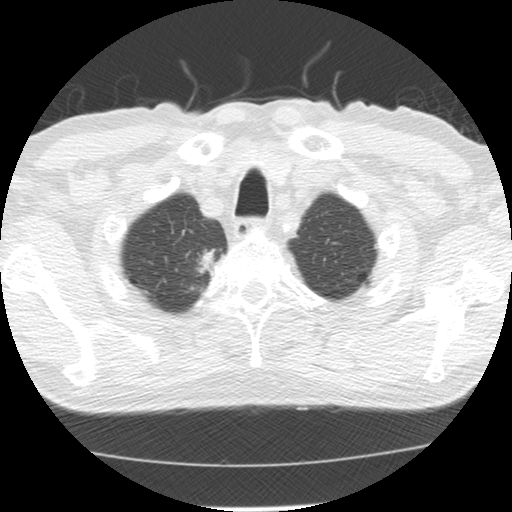
Low-dose screening chest CT, axial slice. Baseline annual screen. Lung window (W 1500 / L -600 HU). Standard (soft-tissue) reconstruction kernel (STANDARD). Slice 20 of 139 in the series. Male participant, aged 64 years at enrolment.
Expert-annotated lung lesion, box from (x=181, y=242) to (x=224, y=282) px. Screening reader's record for this exam (one nodule recorded; not confirmed to be the boxed lesion): non-calcified nodule or mass ≥4 mm, right upper lobe, 20 × 13 mm, spiculated (stellate) margins, soft tissue attenuation. Official screen result: positive, change unspecified: nodule(s) >= 4 mm or enlarging nodule(s), mass(es), or other non-specific abnormalities suspicious for lung cancer. Participant outcome: lung cancer diagnosed 73 days after this screen — adenocarcinoma, NOS, right upper lobe, moderately differentiated (G2), stage IA (AJCC 6th edition), 17 mm at pathology.